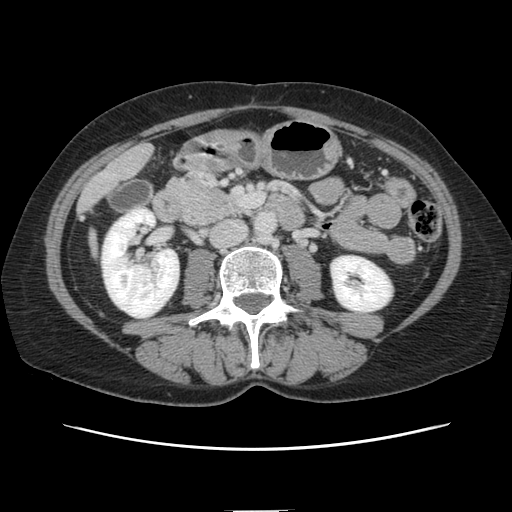
Contrast-enhanced abdominal CT, one axial slice; position 32 of 141 along the scan axis; soft-tissue window (W 400 / L 40 HU); 512 × 512 image matrix. Female patient, age 63 years. Case-level facts recorded for this patient, not image findings: diagnosis: colorectal cancer liver metastases, imaged before liver resection; multiple liver metastases: yes.
Outlined on this slice (outlined manually by an expert reader):
- liver: bounding box <81,145,152,209> (left, top, right, bottom; pixels)